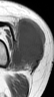
MRI of an extremity soft-tissue mass, one axial slice; position 24 of 42 along the scan axis; MR volume resampled by the dataset authors to the PET/CT grid (not the native acquisition matrix); 3.27 mm slice thickness; 54 × 97 image matrix, field of view 53 × 95 mm. Female patient. From the clinical record (not read from this slice): histological type: spindle cell suggestive of biphasic synovial sarcoma; grade: intermediate; site of the primary tumour: left knee.
Annotated regions visible in this slice (expert contour drawn on MRI and transferred to this co-registered scan by the dataset authors):
- gross tumour volume including surrounding oedema: box from (x=14, y=16) to (x=43, y=68) px
- gross tumour volume (mass): (x=15, y=19)–(x=43, y=68)